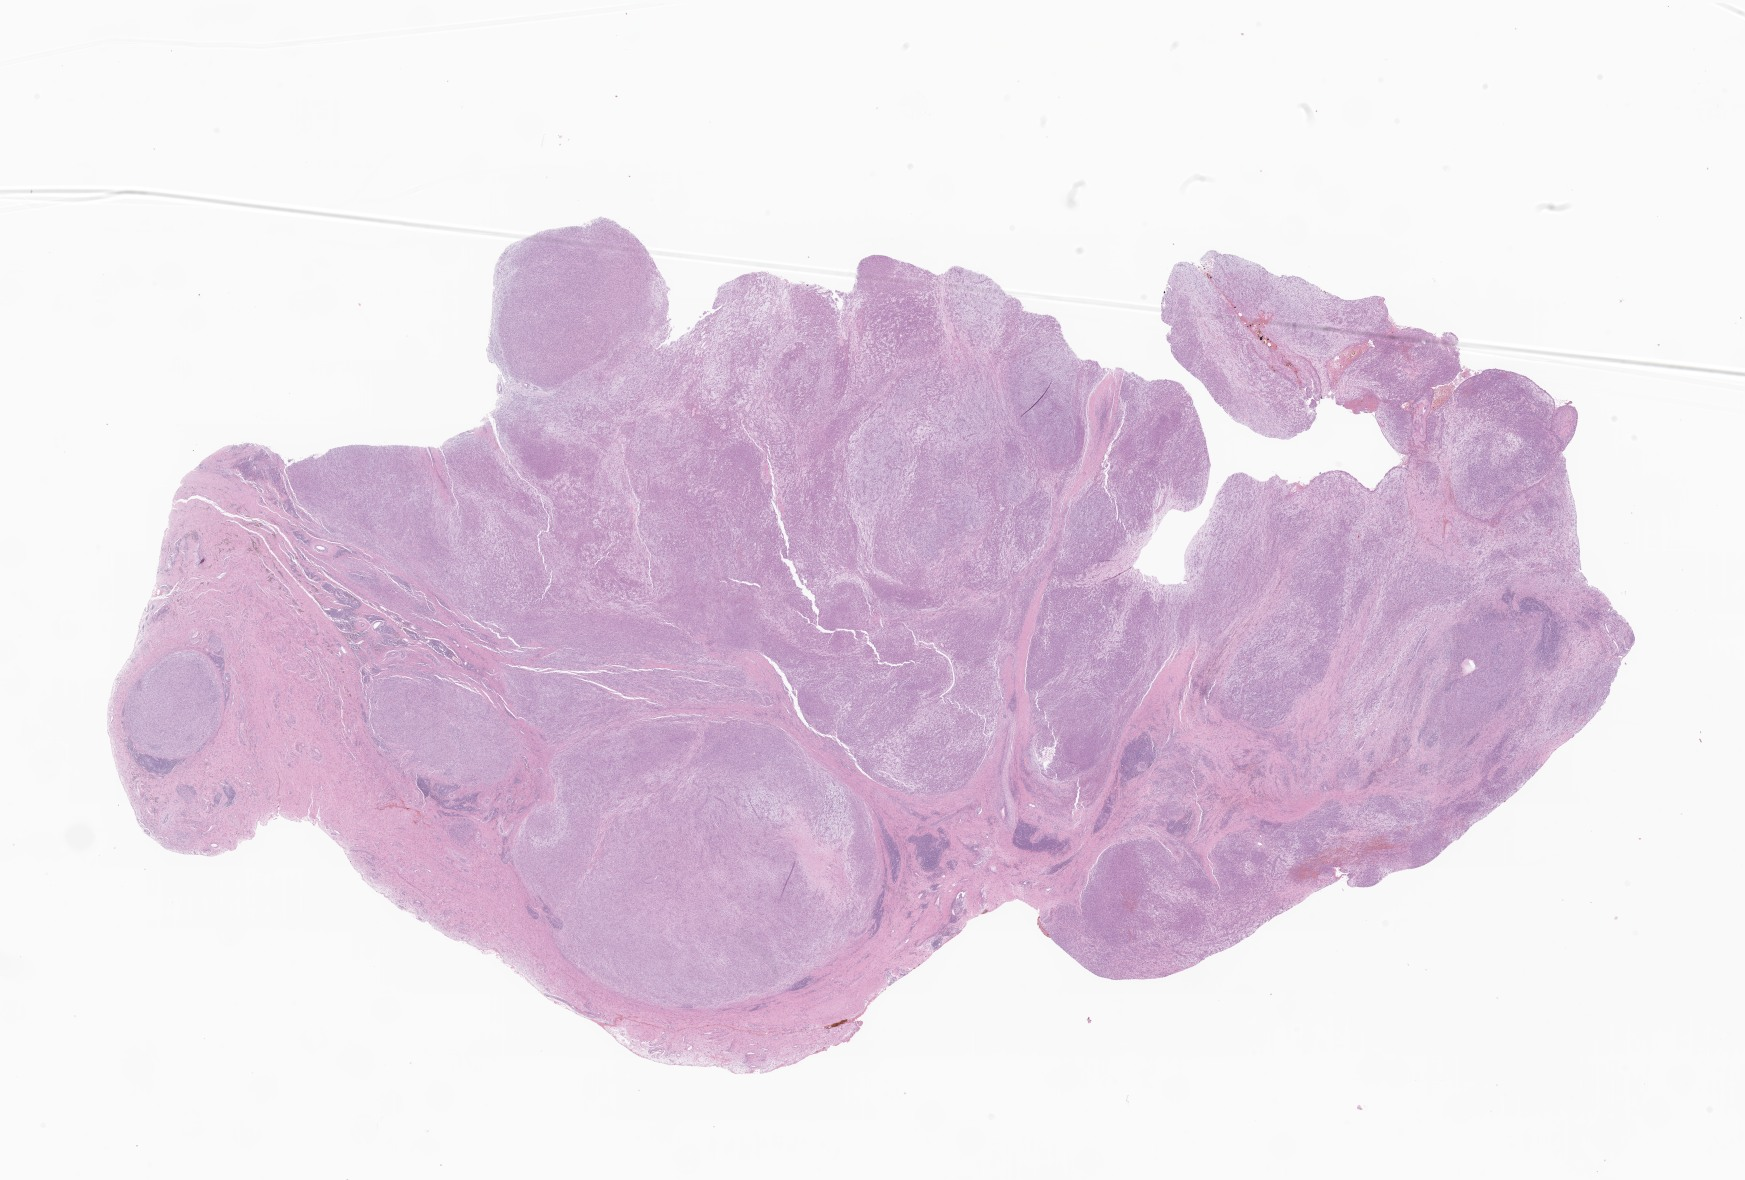
Digitized H&E-stained section of tumor tissue from the soft tissue of lower extremity, whole scanned area (about 29.4 x 19.9 mm) shown as a low-resolution overview; FFPE section. Female patient, age 167 months (13 years 11 months).
Diagnosis: Angiomatoid fibrous histiocytoma.